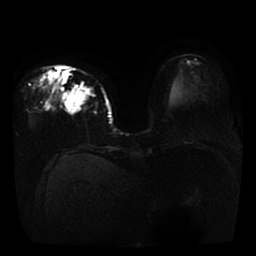
Breast MRI, one axial slice. Position 14 of 41 along the scan axis. Diffusion-weighted series; image 2 of 4 stored at this slice position (different b-values; order by instance number). 1.5 T. 5 mm slice thickness. 256 × 256 image matrix, field of view 330 × 330 mm. Female patient.
Annotated regions visible in this slice (outlined manually by an expert reader):
- tumour on diffusion-weighted imaging: box from (x=67, y=89) to (x=89, y=109) px